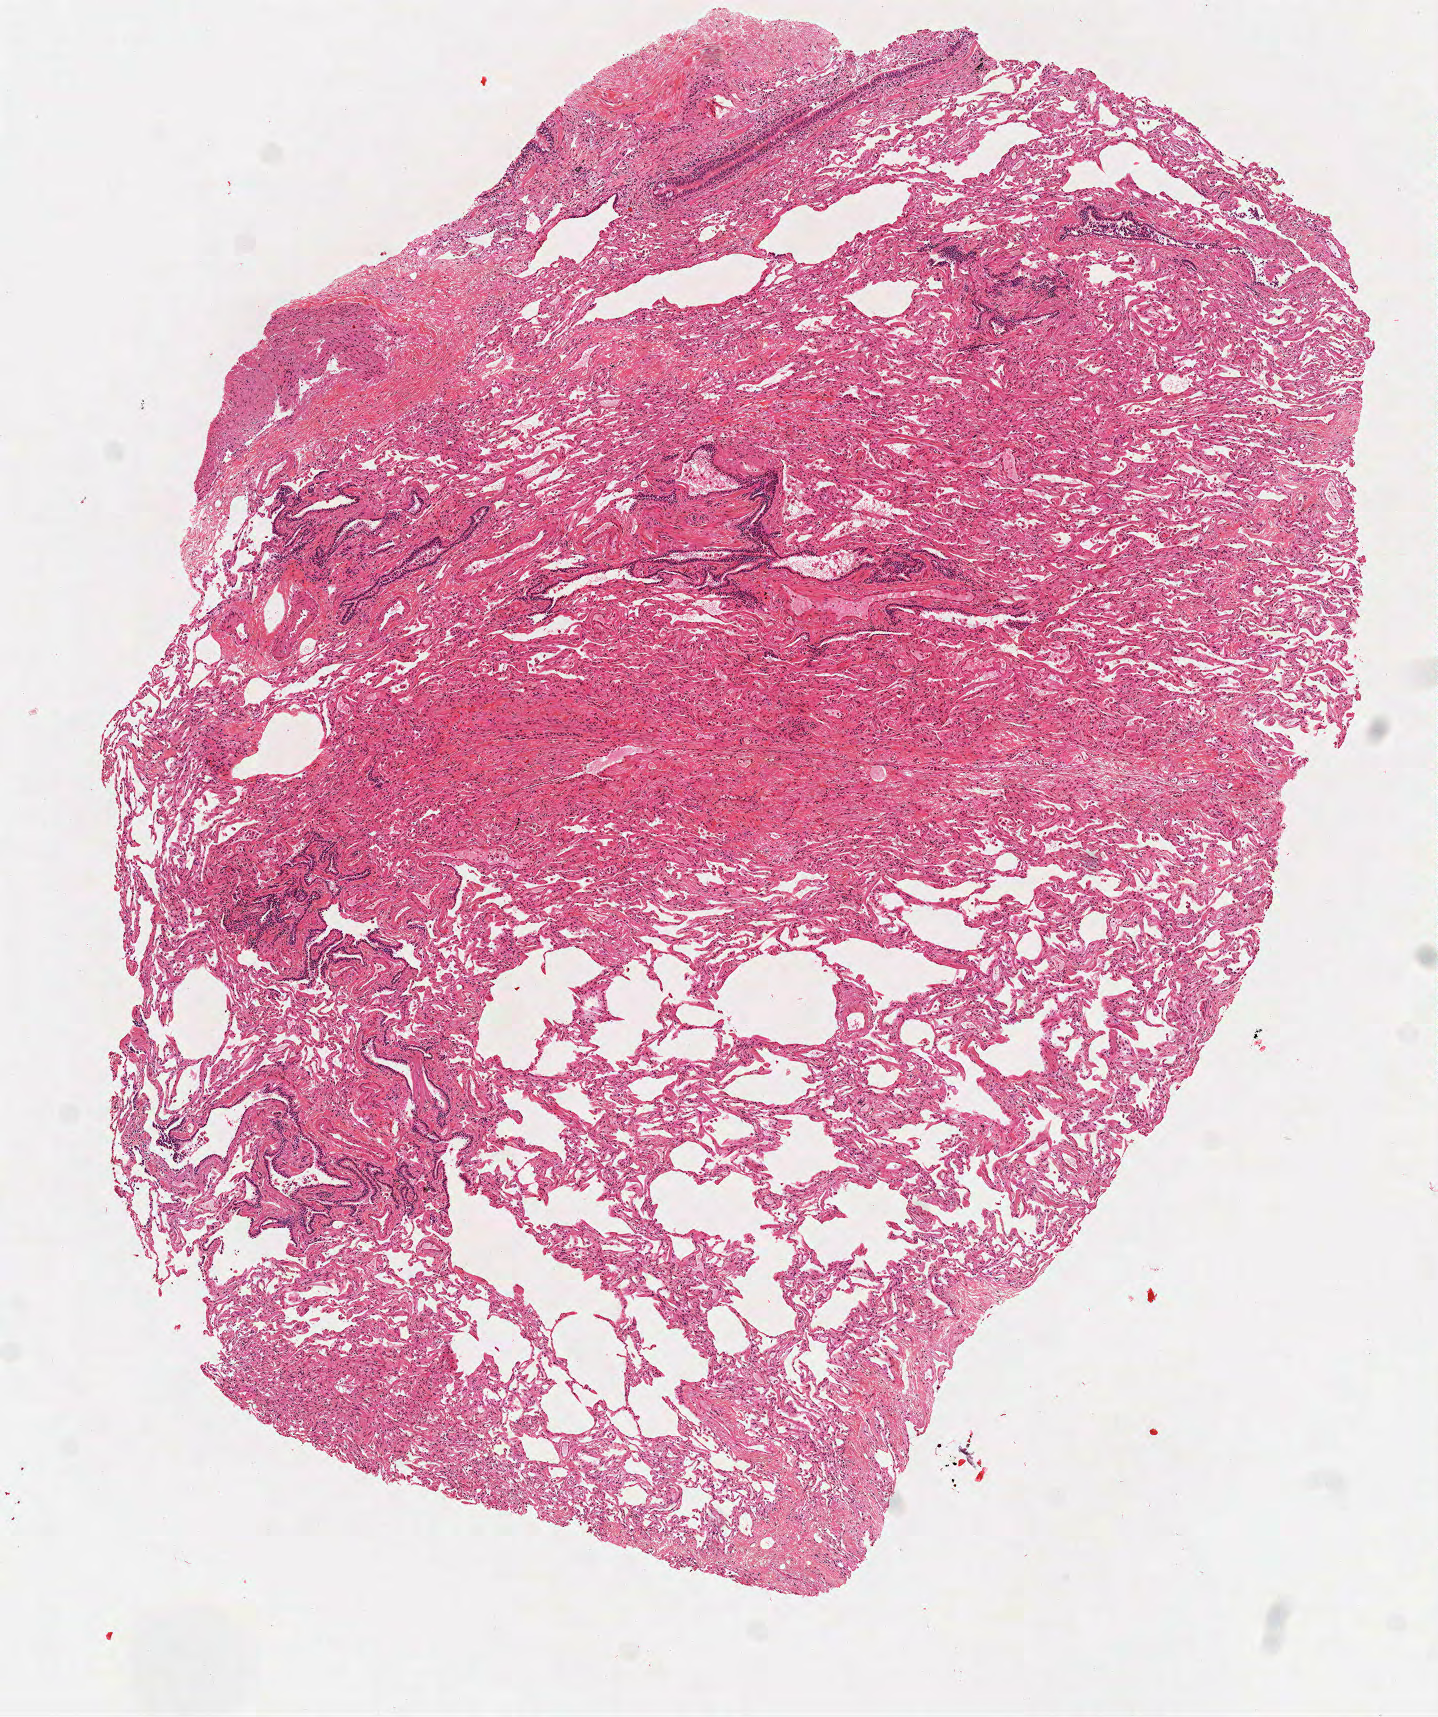
Whole-slide histology image, H&E — whole scanned area (about 5.8 x 6.9 mm, acquisition: 40x scan) shown as a low-resolution overview; frozen section; solid tissue normal (non-tumour tissue) sample from the lung. Female patient; age at initial diagnosis 69 years.
- this section: solid tissue normal sample (biorepository sample class)
- patient diagnosis: Squamous cell carcinoma, NOS (upper lobe, lung)